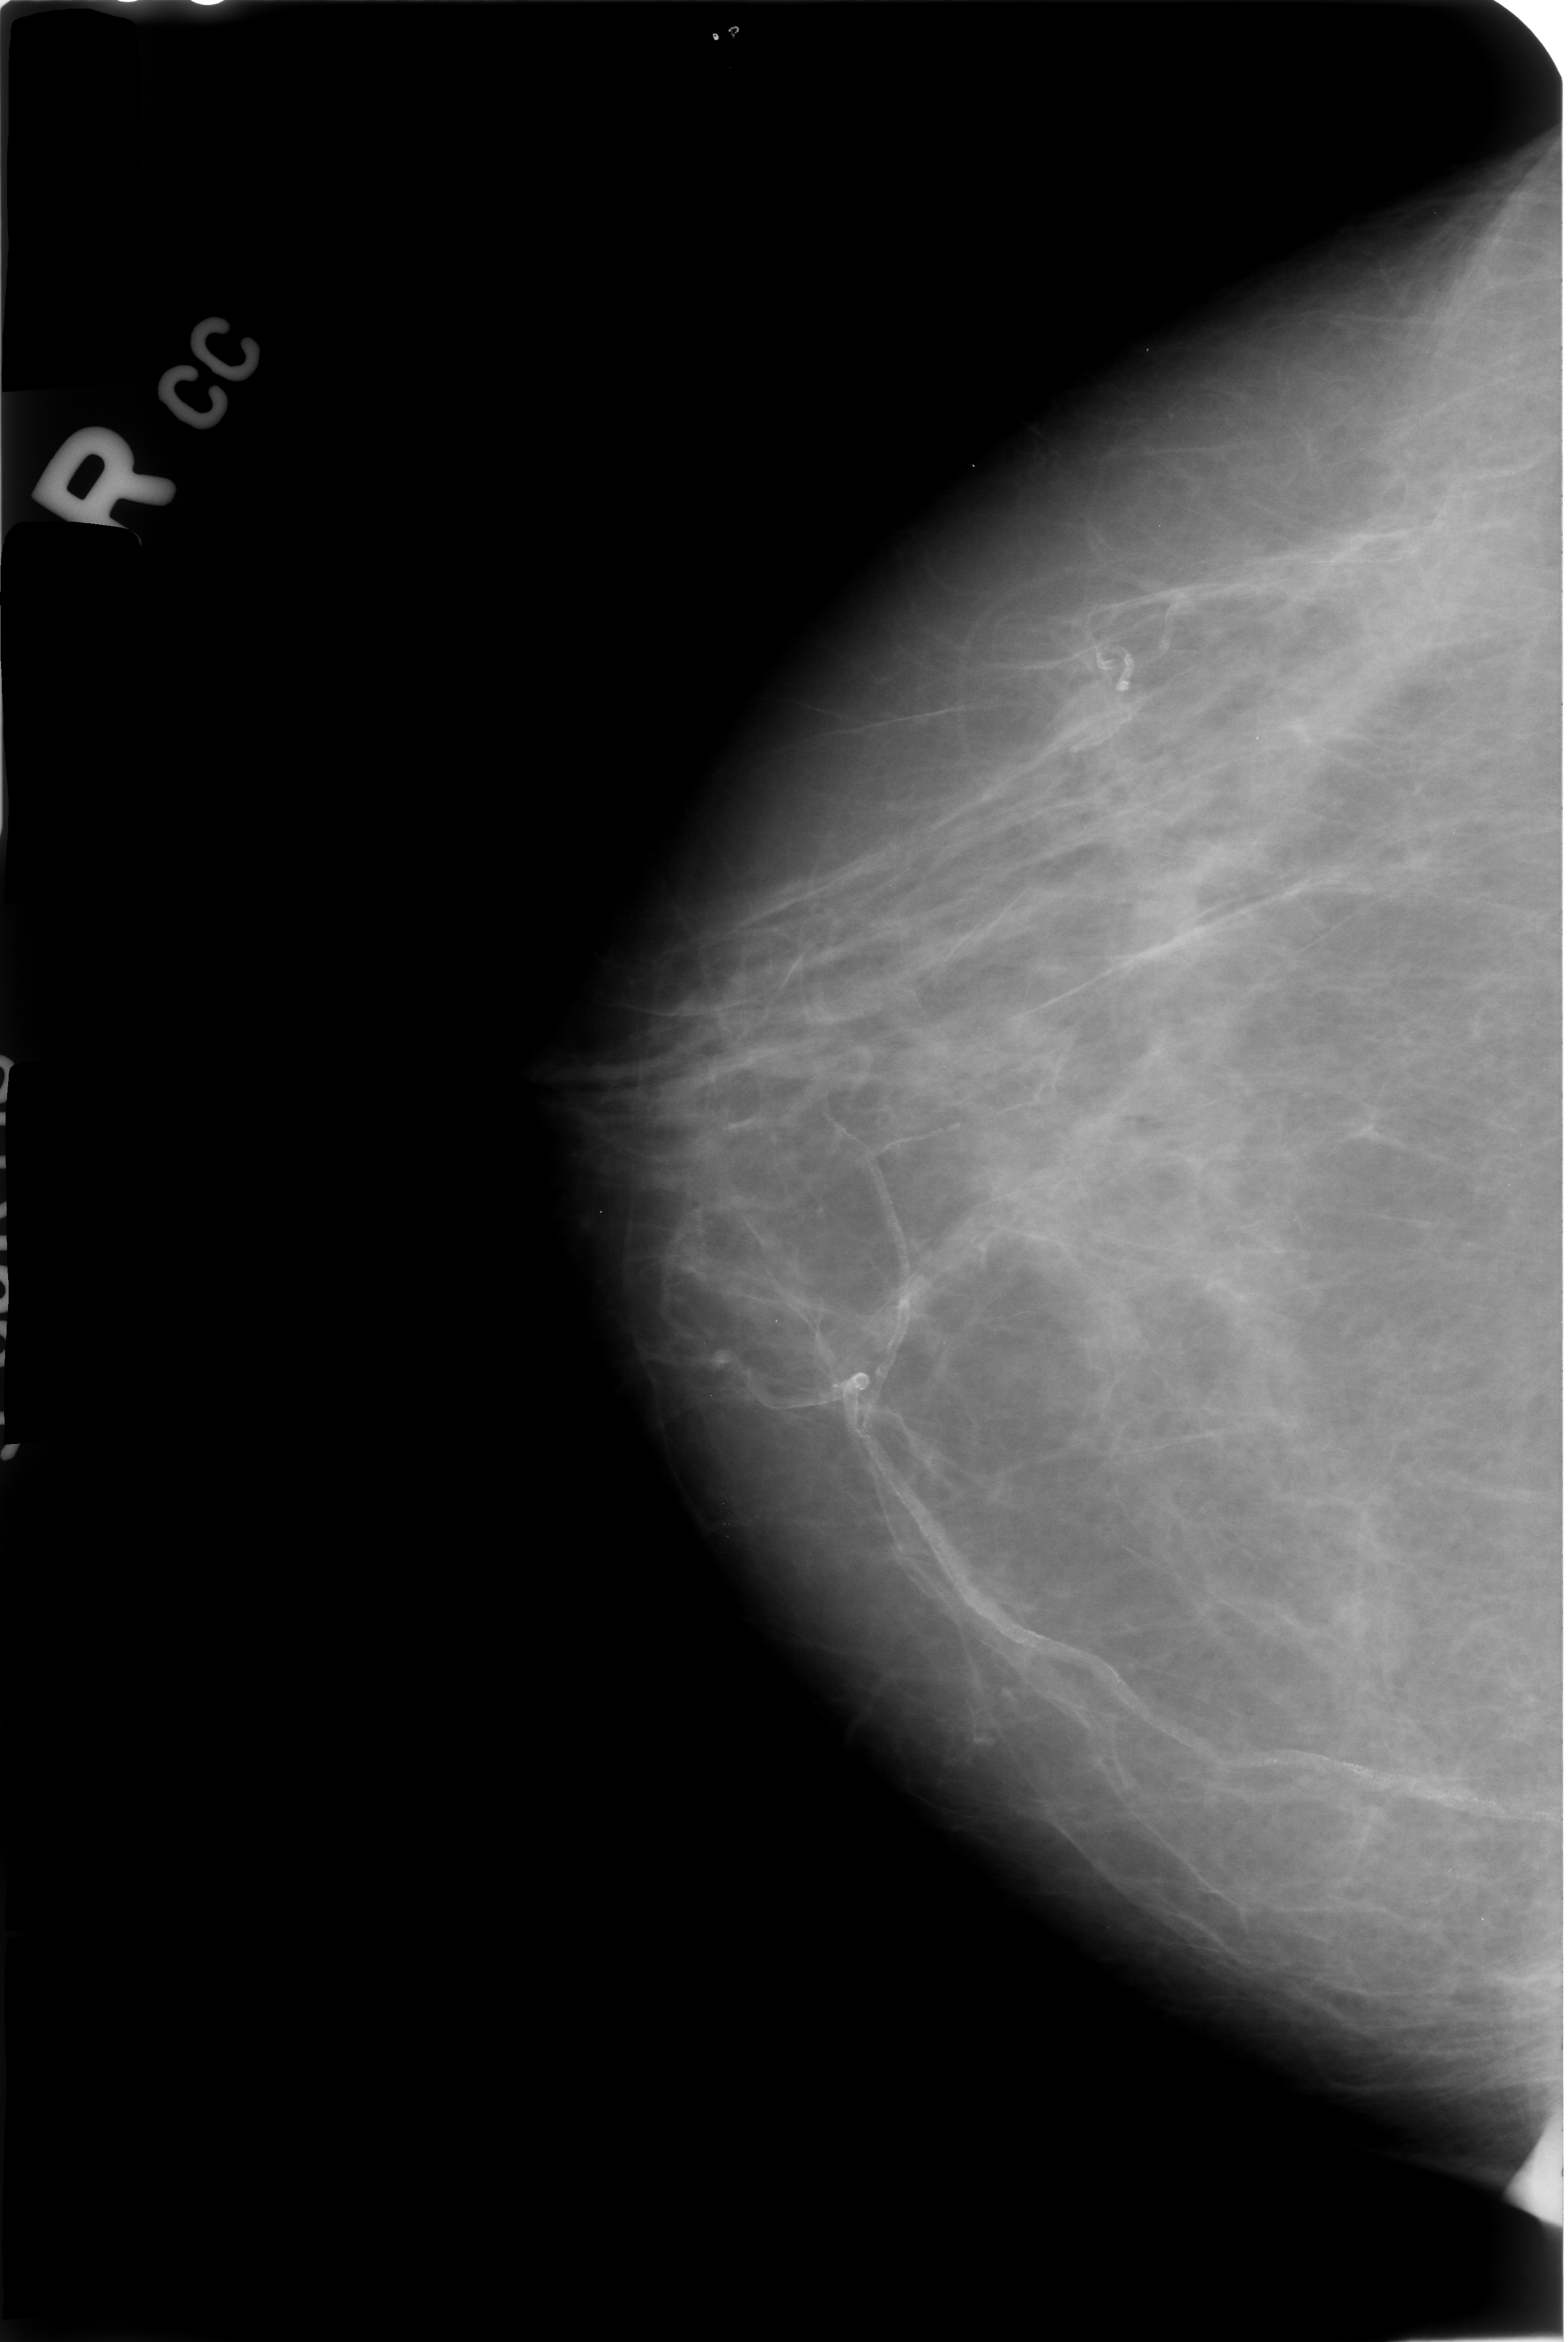
Digitized screen-film mammogram; right breast; craniocaudal (CC) view.
Marked findings (only marked abnormalities are described; nothing is implied about the rest of the image): Finding 1 of 2: calcifications, morphology vascular; BI-RADS assessment category 2; benign; no additional work-up was recommended (benign without callback). Finding 2 of 2: calcifications, morphology vascular; BI-RADS assessment category 2; subtlety rating 3 on a 1 (subtle) to 5 (obvious) scale; benign; no additional work-up was recommended (benign without callback).